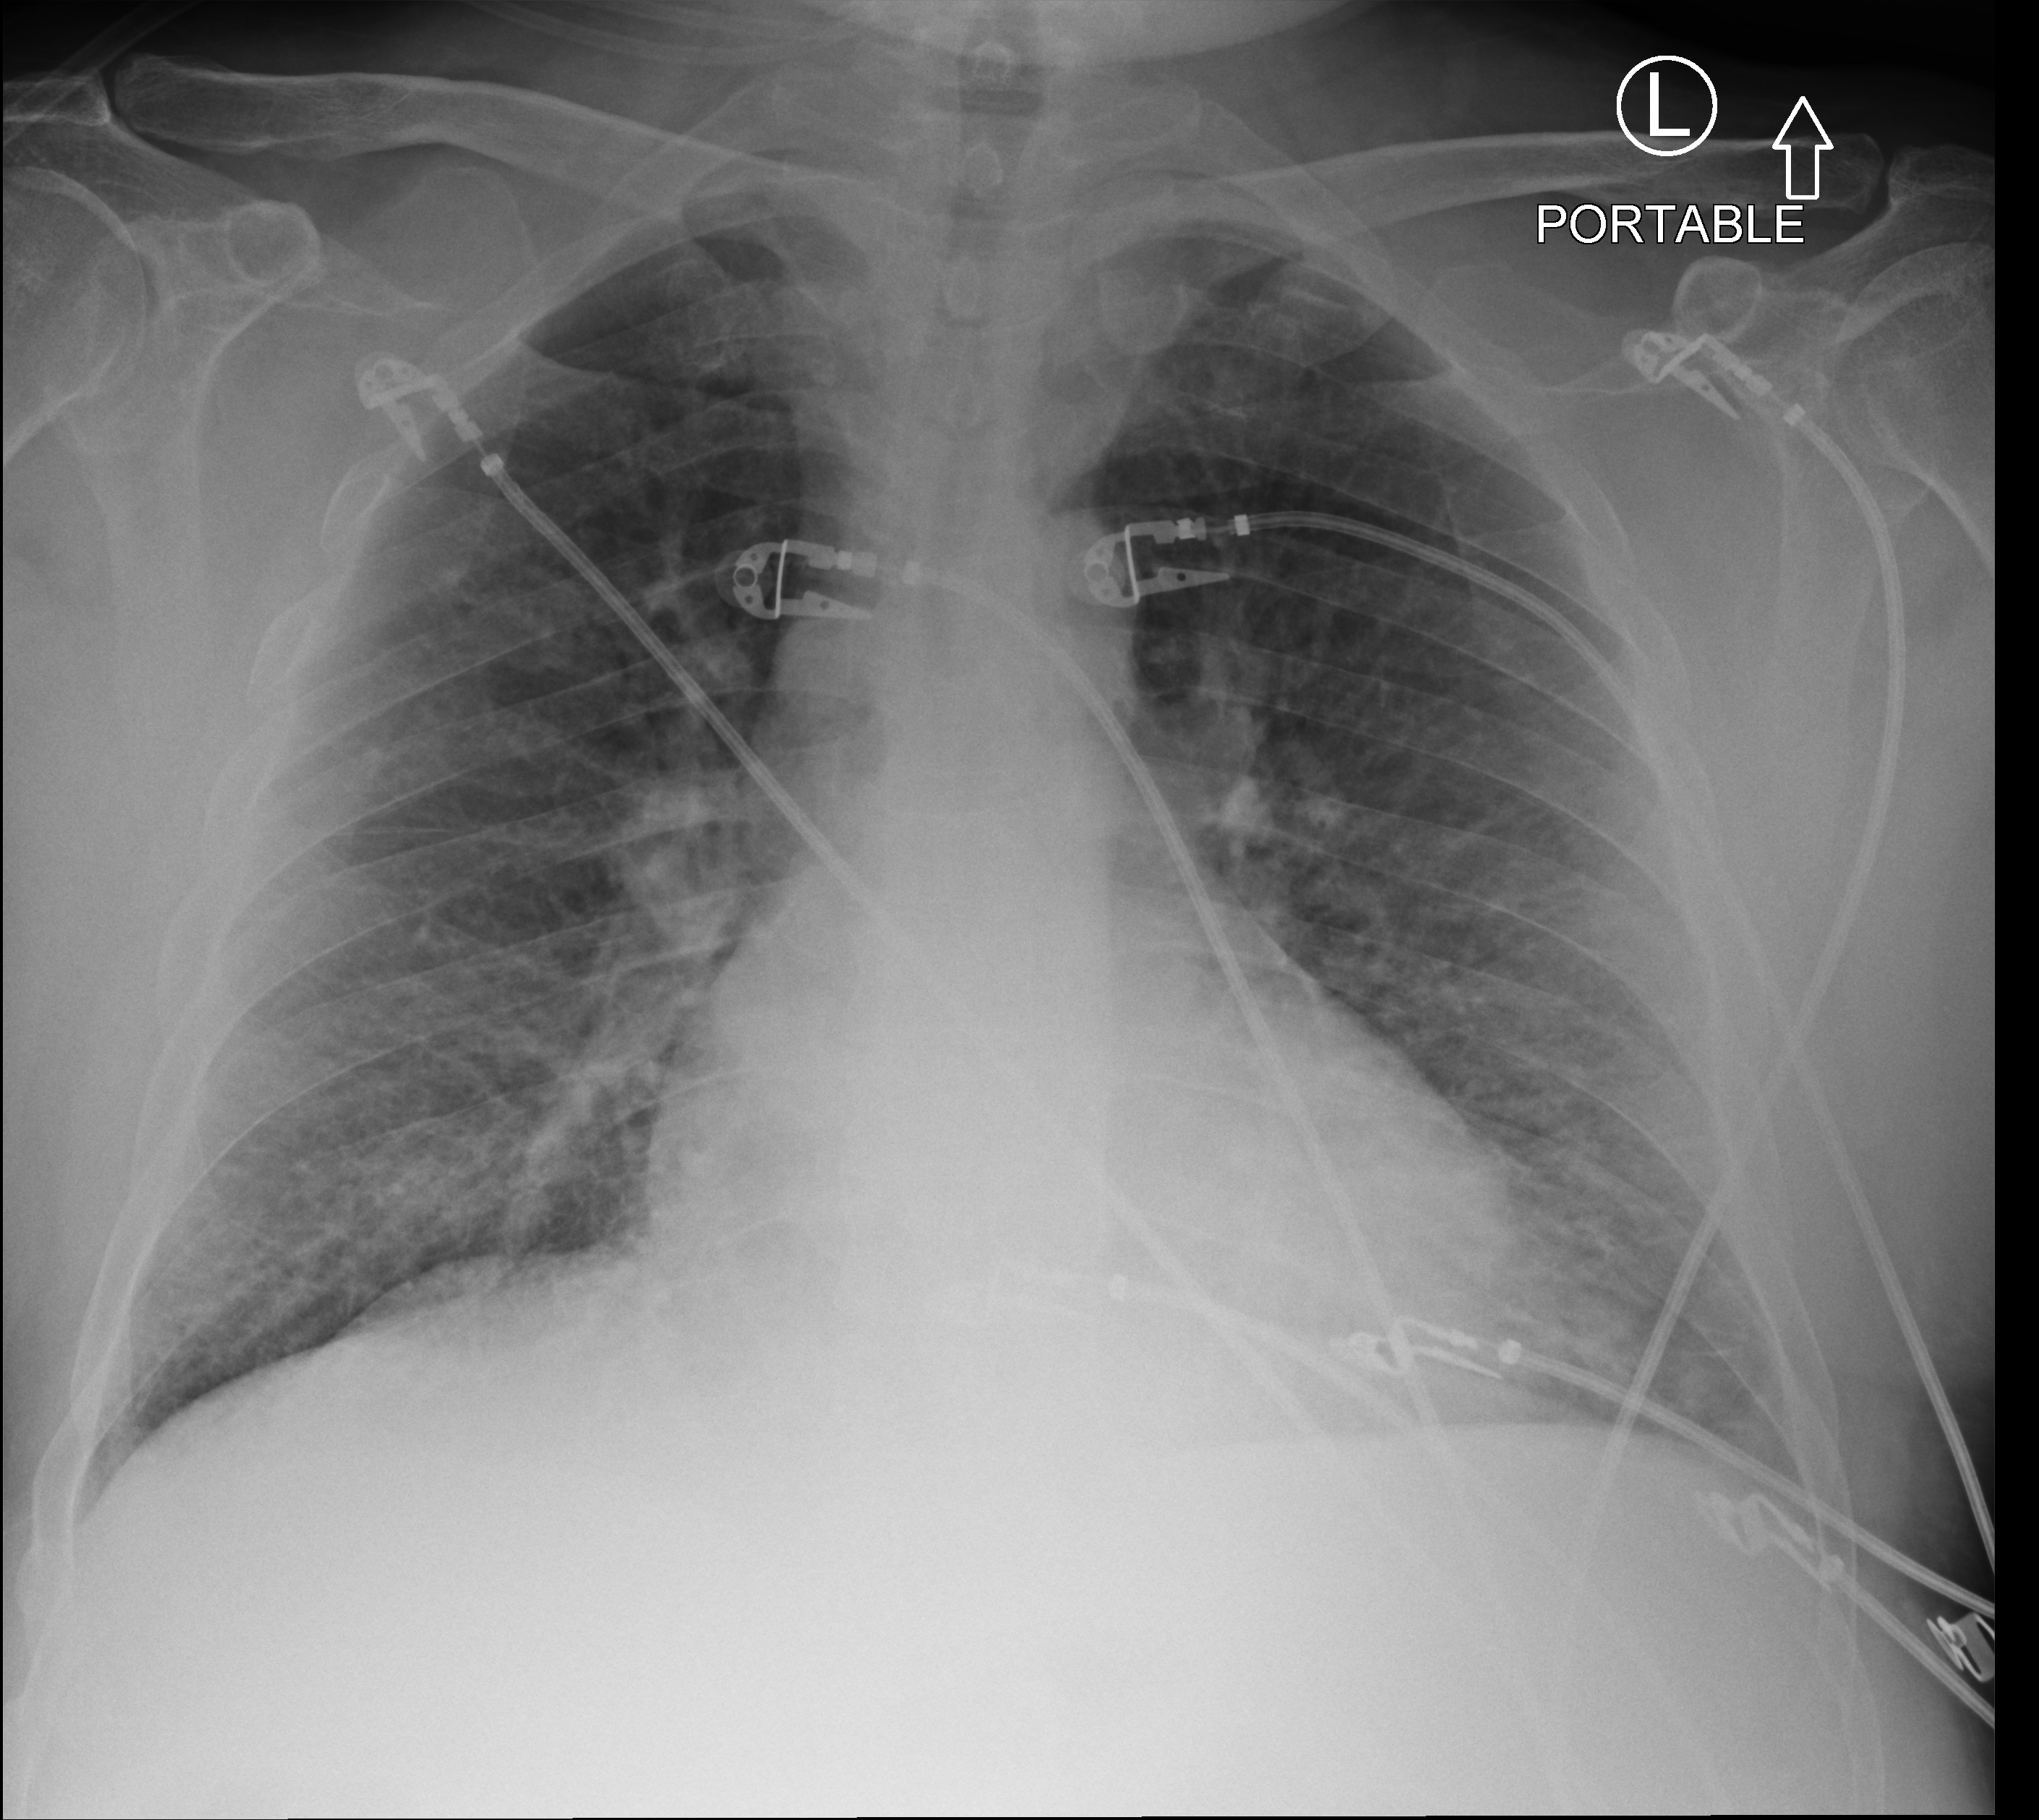
Portable chest radiograph. Male patient hospitalised with COVID-19, age 60–74 years.
From the hospital-stay record, not from the radiograph (when in the stay this image was taken is not recorded):
- mechanically ventilated during this hospital stay: no